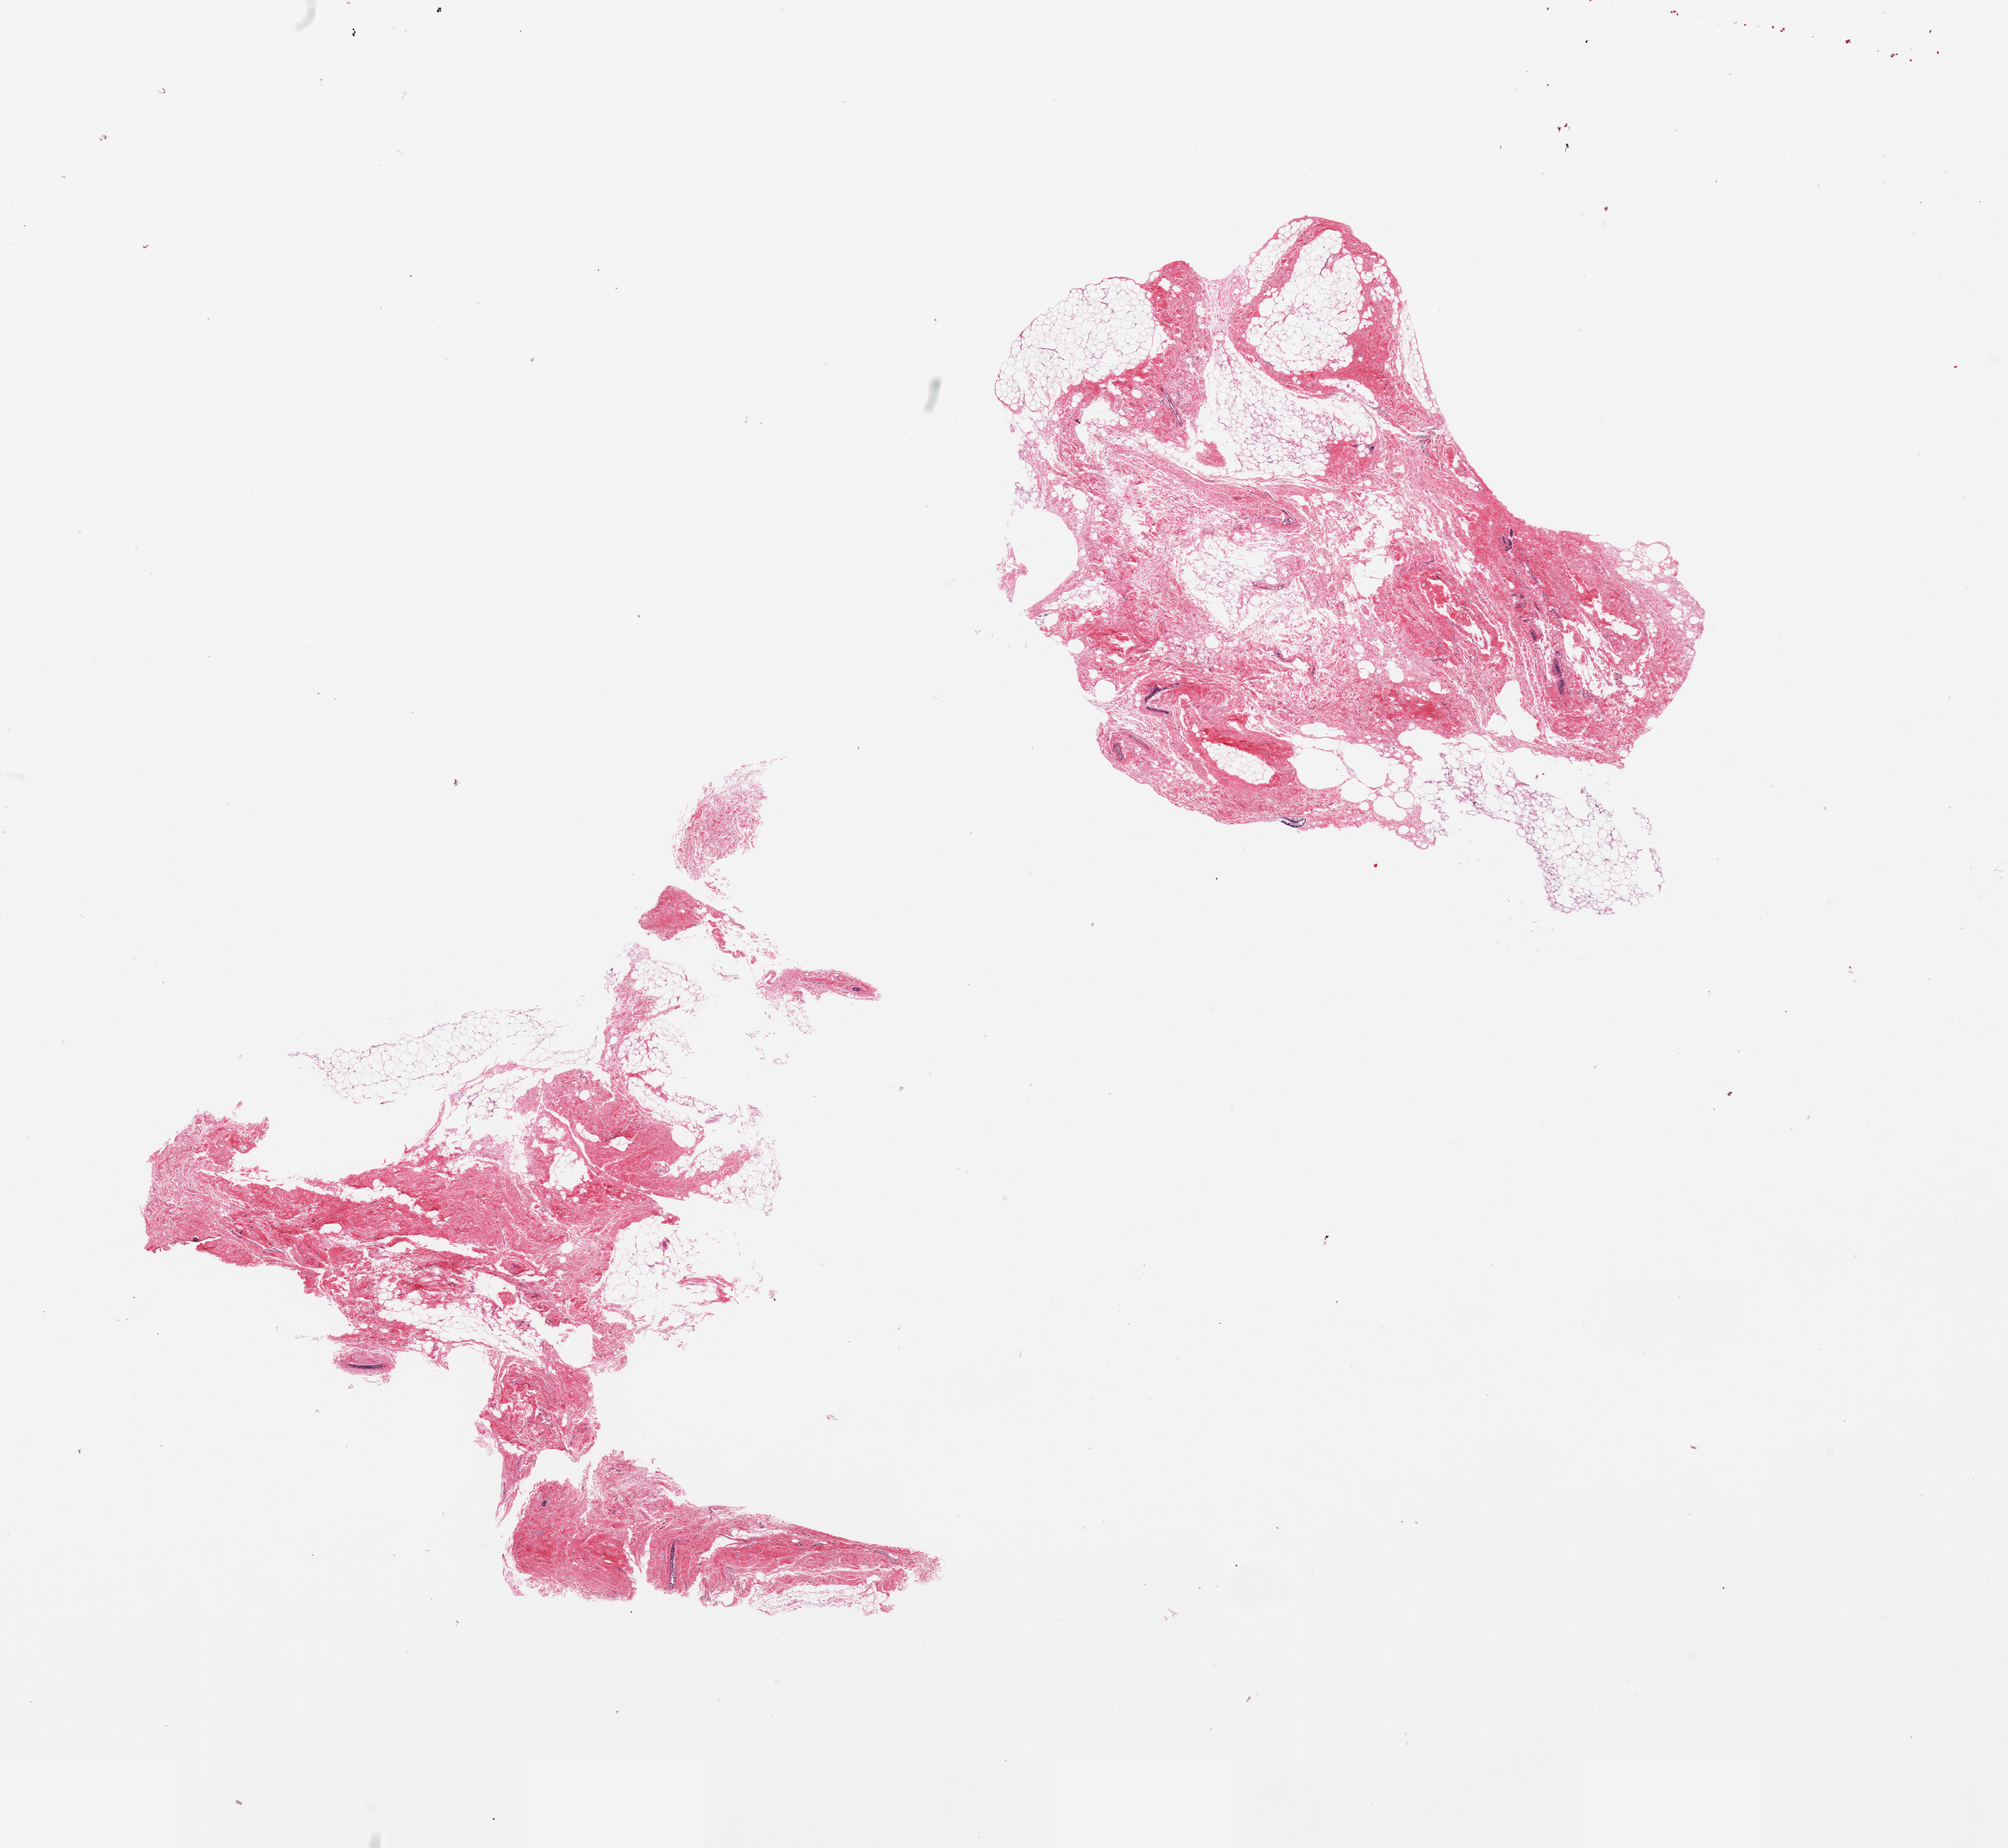
H&E whole-slide image, brightfield, whole scanned area (about 21.7 x 19.9 mm, from a 20x scan) shown as a low-resolution overview; PAXgene-fixed paraffin-embedded (PFPE) section; sampled site (target tissue): breast; tissue donor sample. Female donor.
Review note (as recorded): 2 pieces, ~70% loose fibrous tissue, epithelium is <5%, small floater (colonic gland).